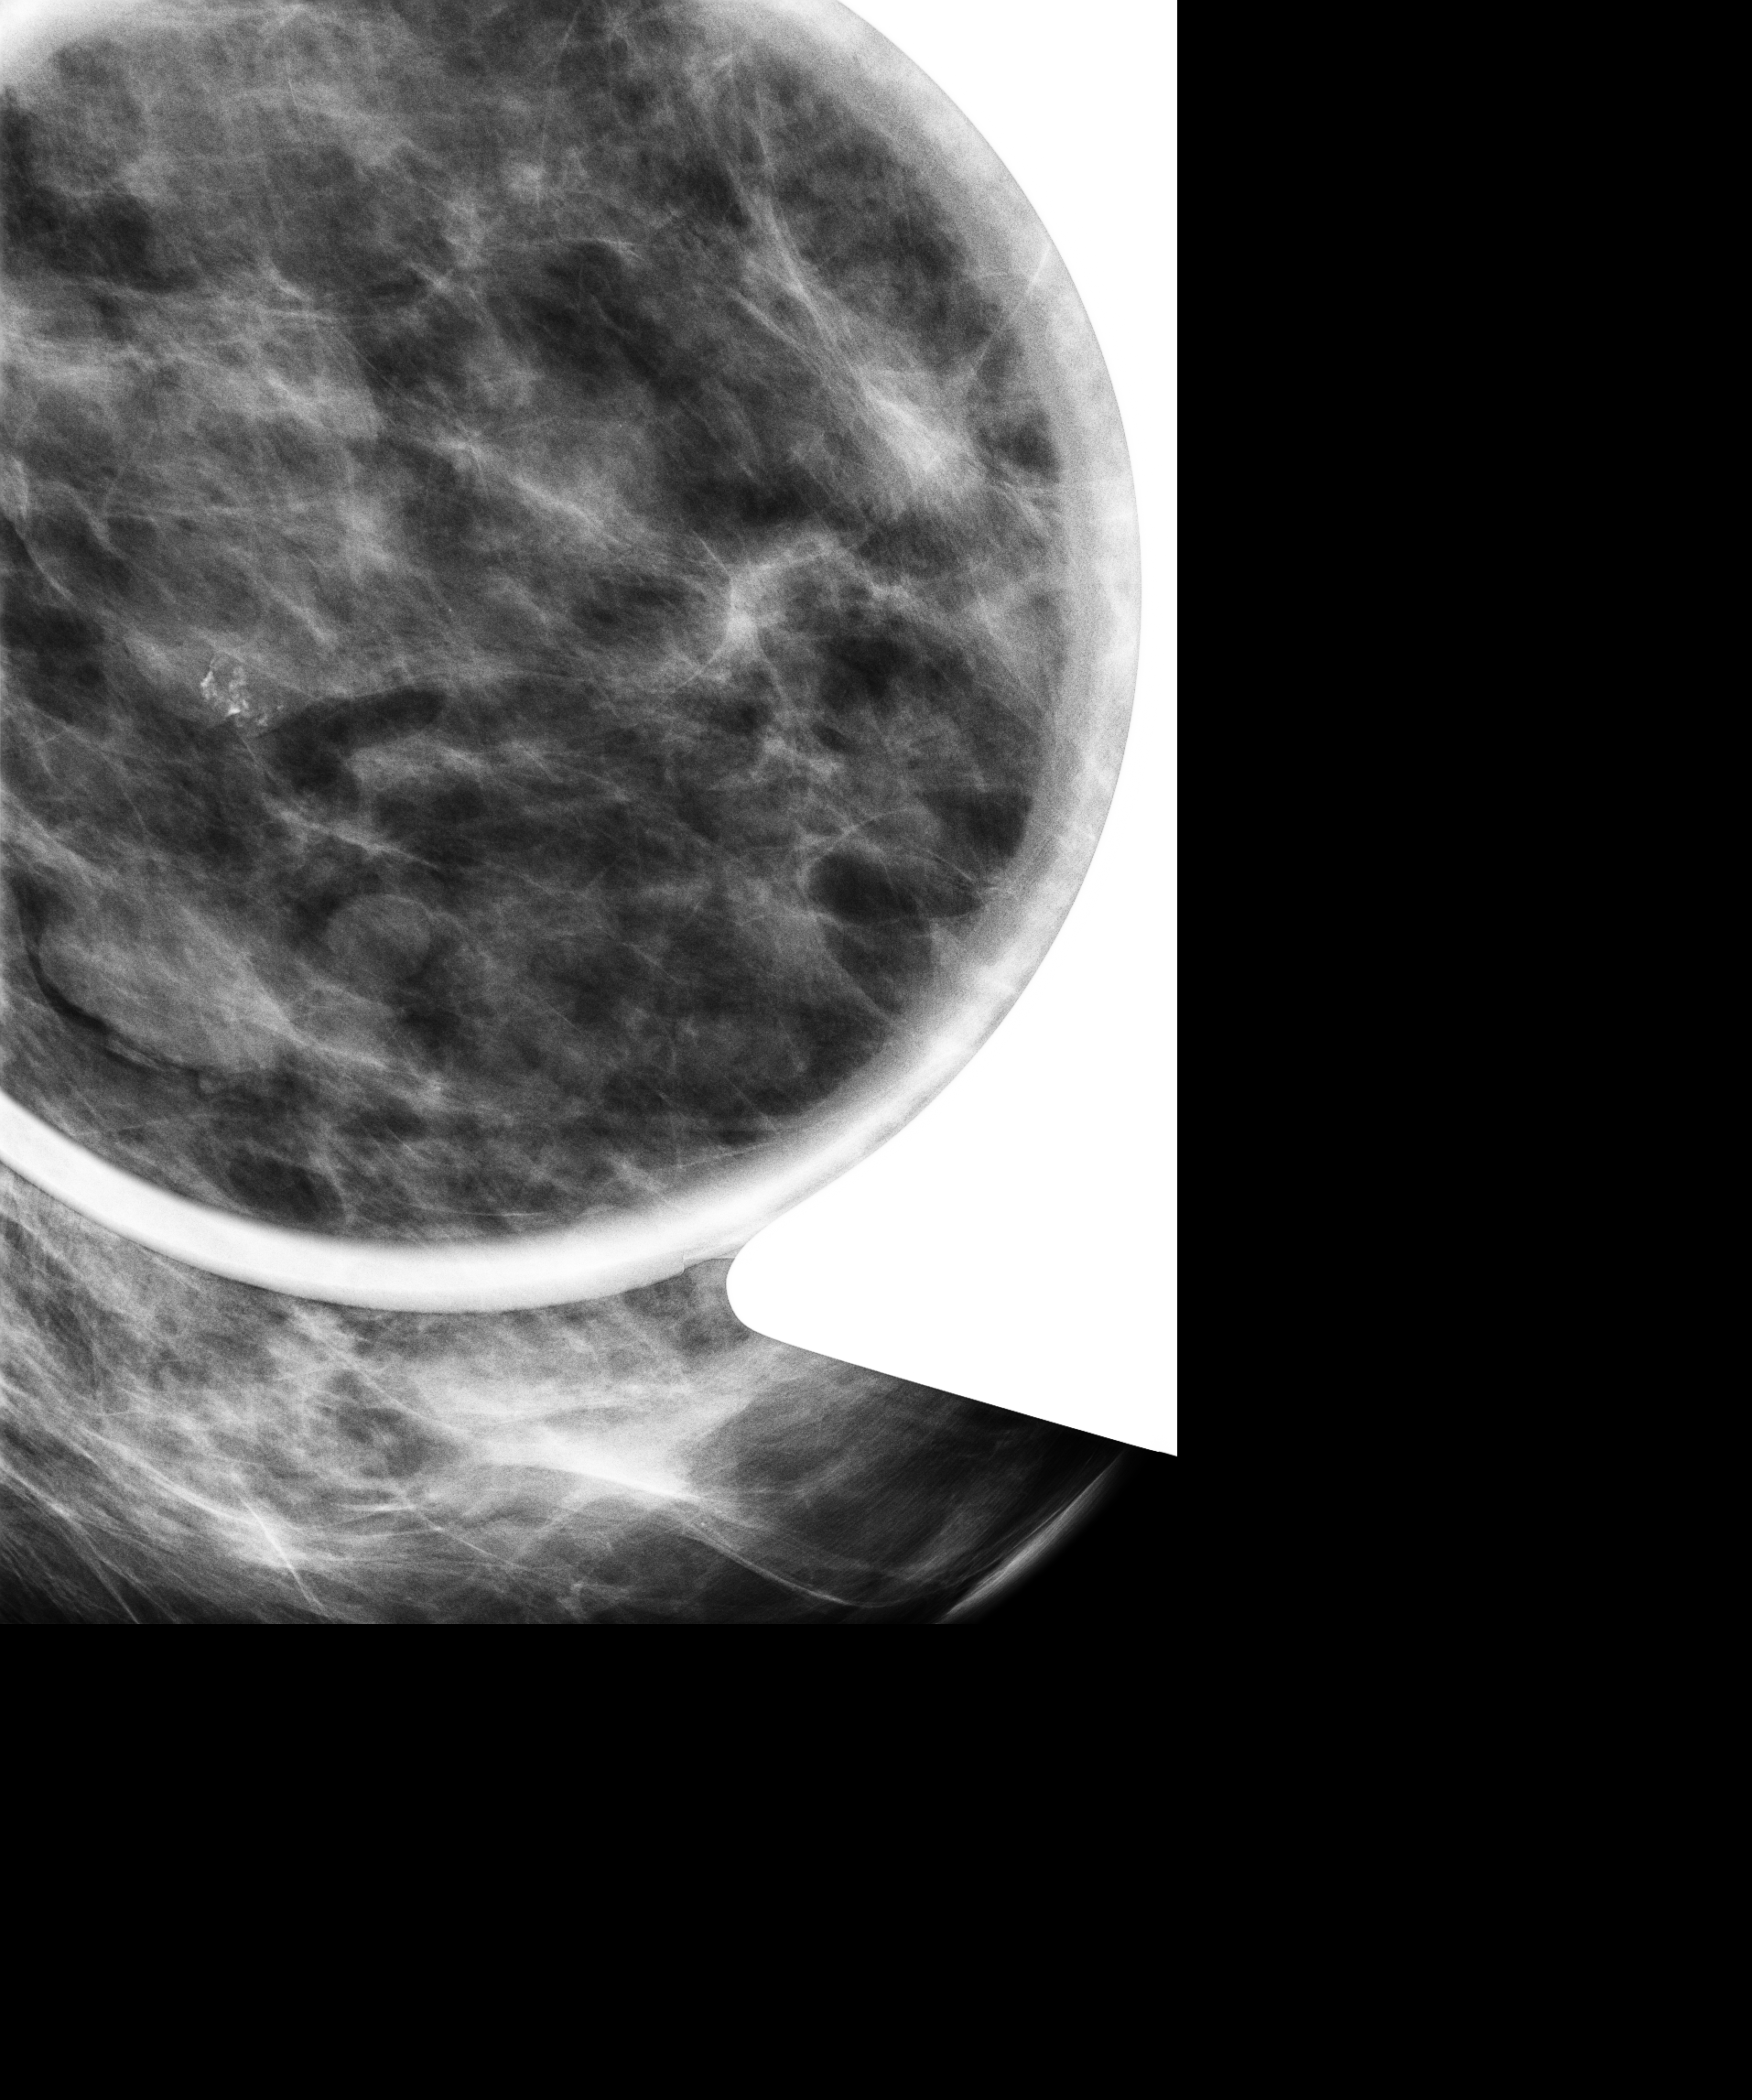
Diagnostic examination (additional views); compressed breast thickness 53.2 mm. Patient: female, 52 years.
Image type: full-field digital mammogram. Breast: left. Projection: LM view.